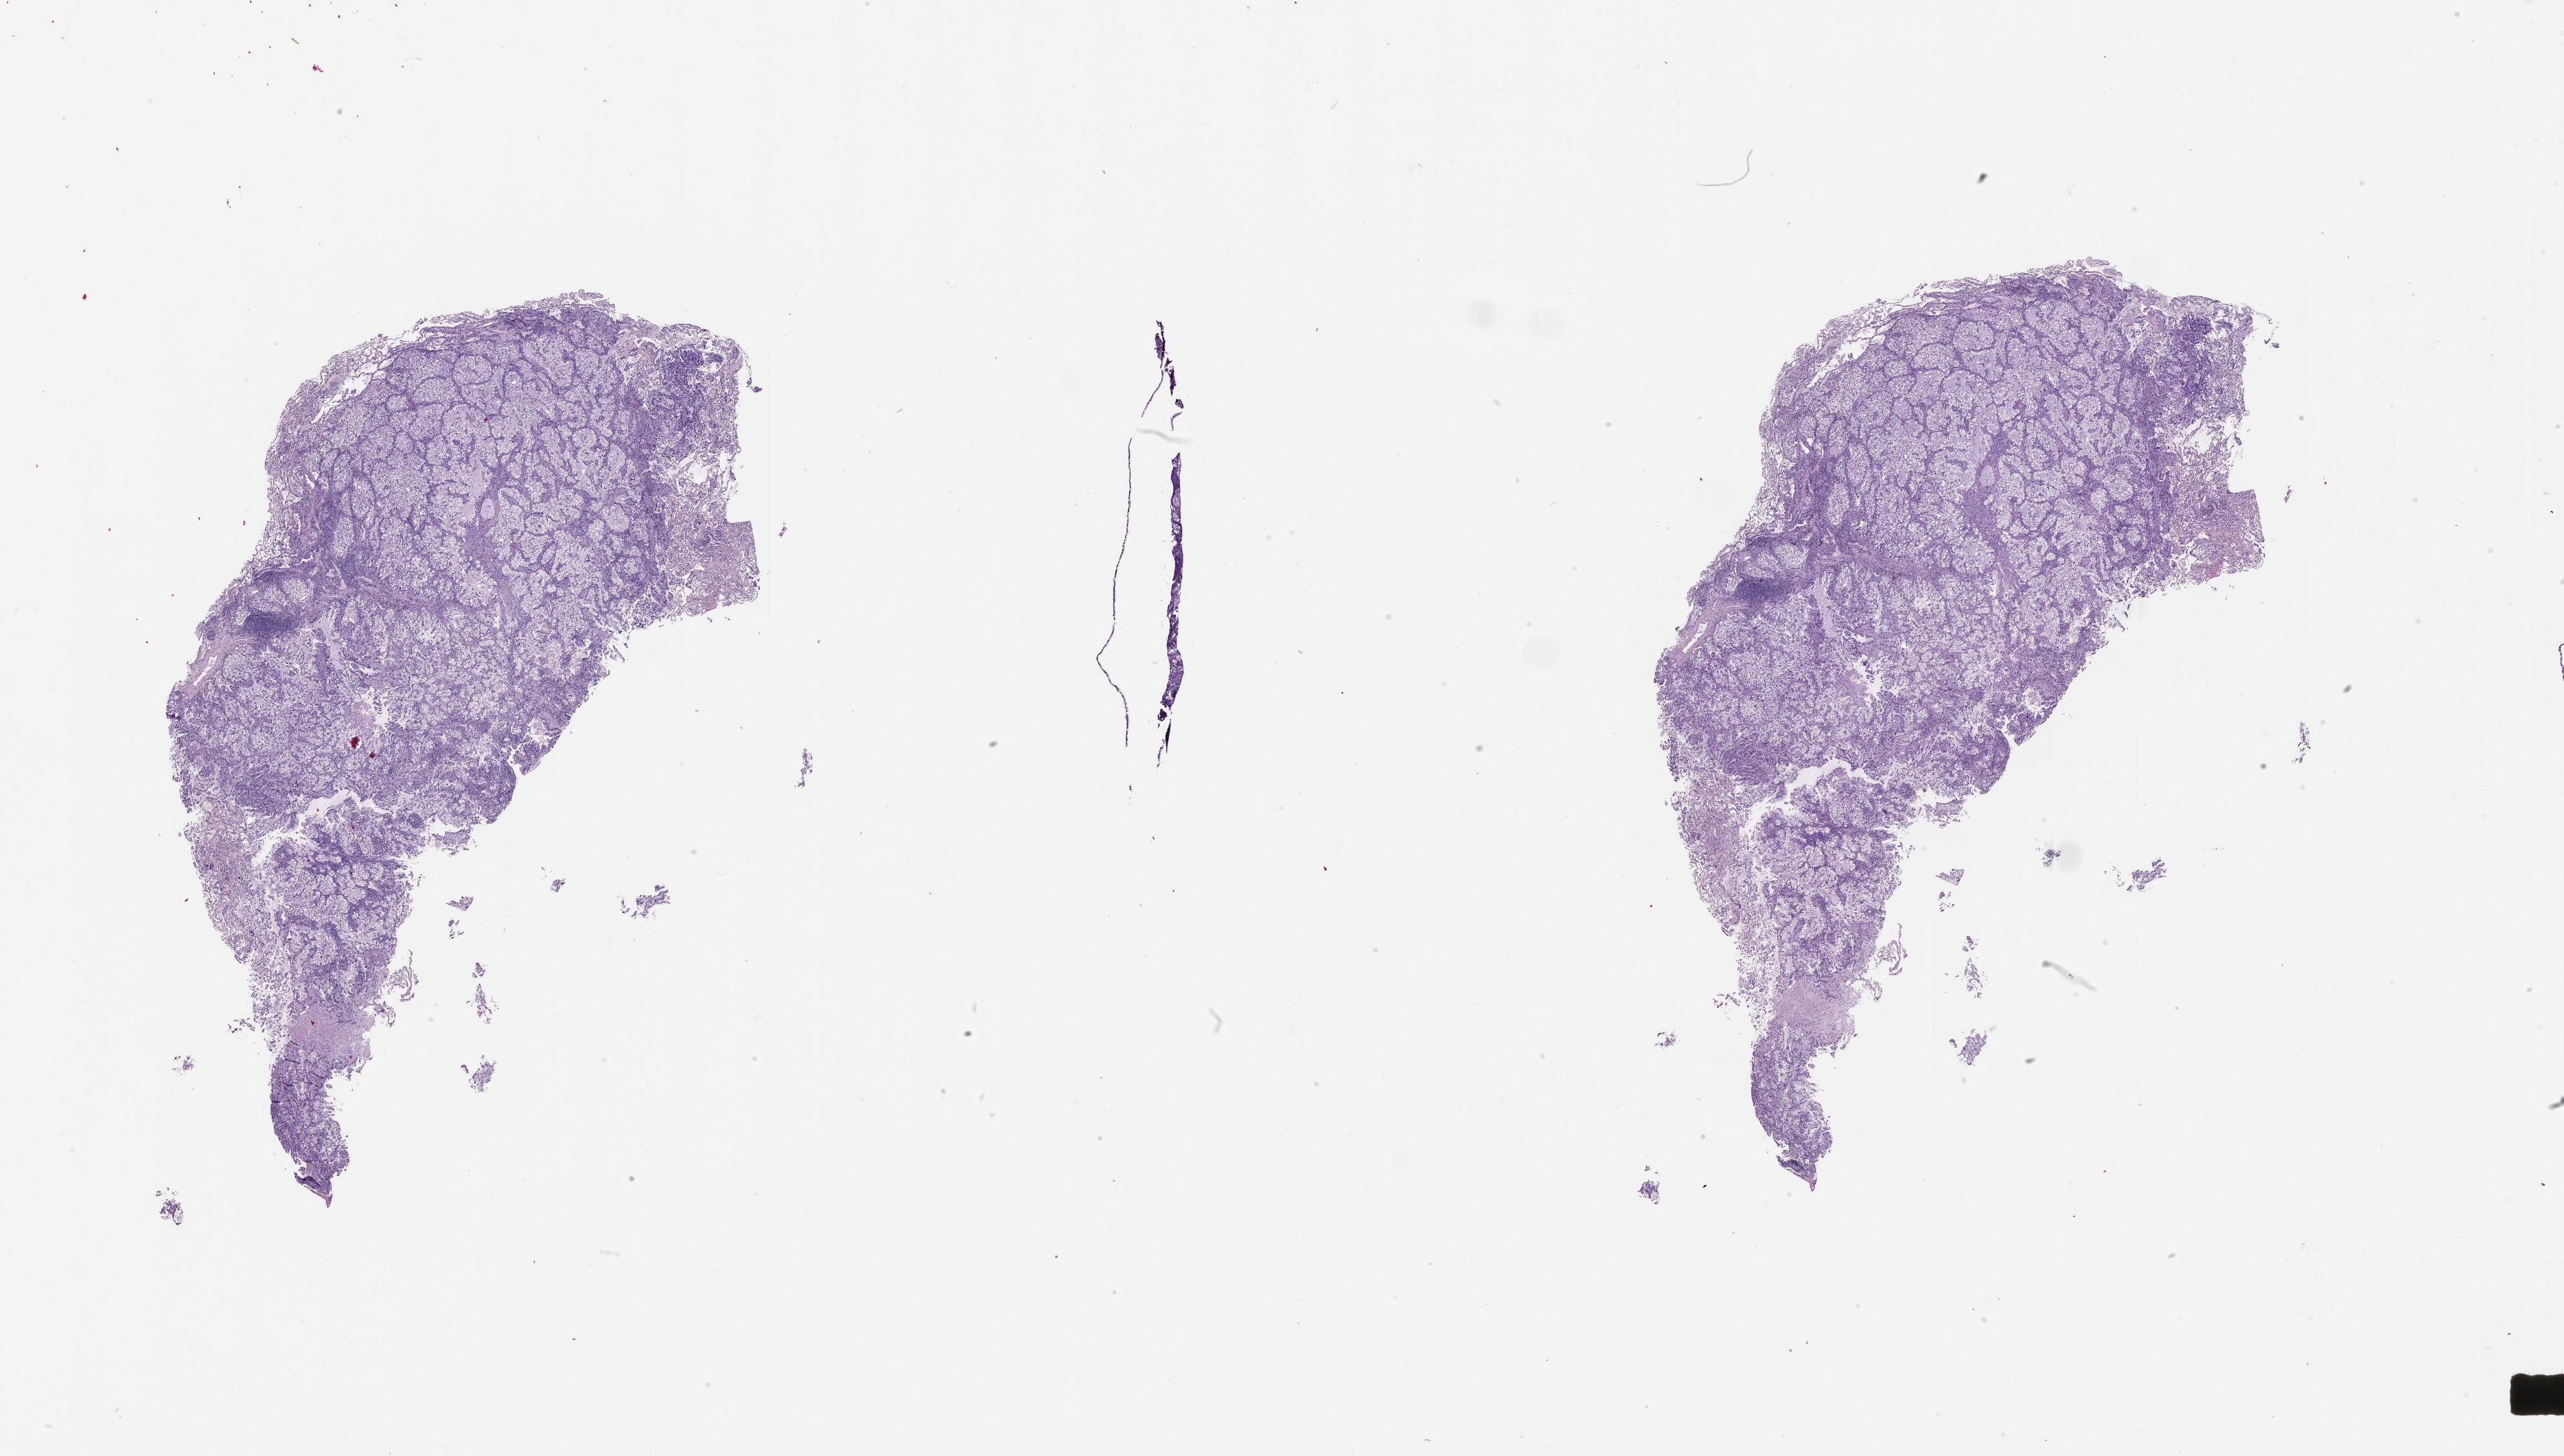
H&E whole-slide image, whole scanned area (about 30.1 x 17.1 mm, acquisition: 20x scan) shown as a low-resolution overview, tumour tissue sample, sampled site: lung. Patient: male, age 67 years. Histologic grade: G2 (moderately differentiated). Slide review estimates, as recorded: tumour nuclei 70%, necrosis 7%.
Diagnosis: Adenocarcinoma, NOS. AJCC pathologic stage: IA.